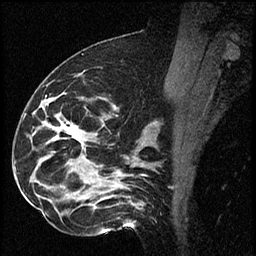
Breast MRI (dynamic contrast-enhanced), one sagittal slice. Slice 35 of 60 in the series (ordered by position). Dynamic contrast-enhanced series, image 2 of 2 at this slice position (ordered by acquisition). 1.5 T. TE 4.2 ms, TR 17.3 ms. 2 mm slice thickness. 256 × 256 image matrix, field of view 200 × 200 mm. Female patient. From the clinical record (not read from this slice): setting: breast cancer imaged before/during neoadjuvant chemotherapy; receptor status: HR-positive, HER2-negative.
Outlined on this slice (semi-automatic segmentation, software-assisted and operator-edited):
- analysis volume of interest (the breast-tissue region the enhancement analysis was run in; not a lesion): bounding box <41,96,115,223> (left, top, right, bottom; pixels)
- tumour enhancement mask (voxels above the 100 % enhancement threshold inside the analysis volume of interest): <61,126,82,142>